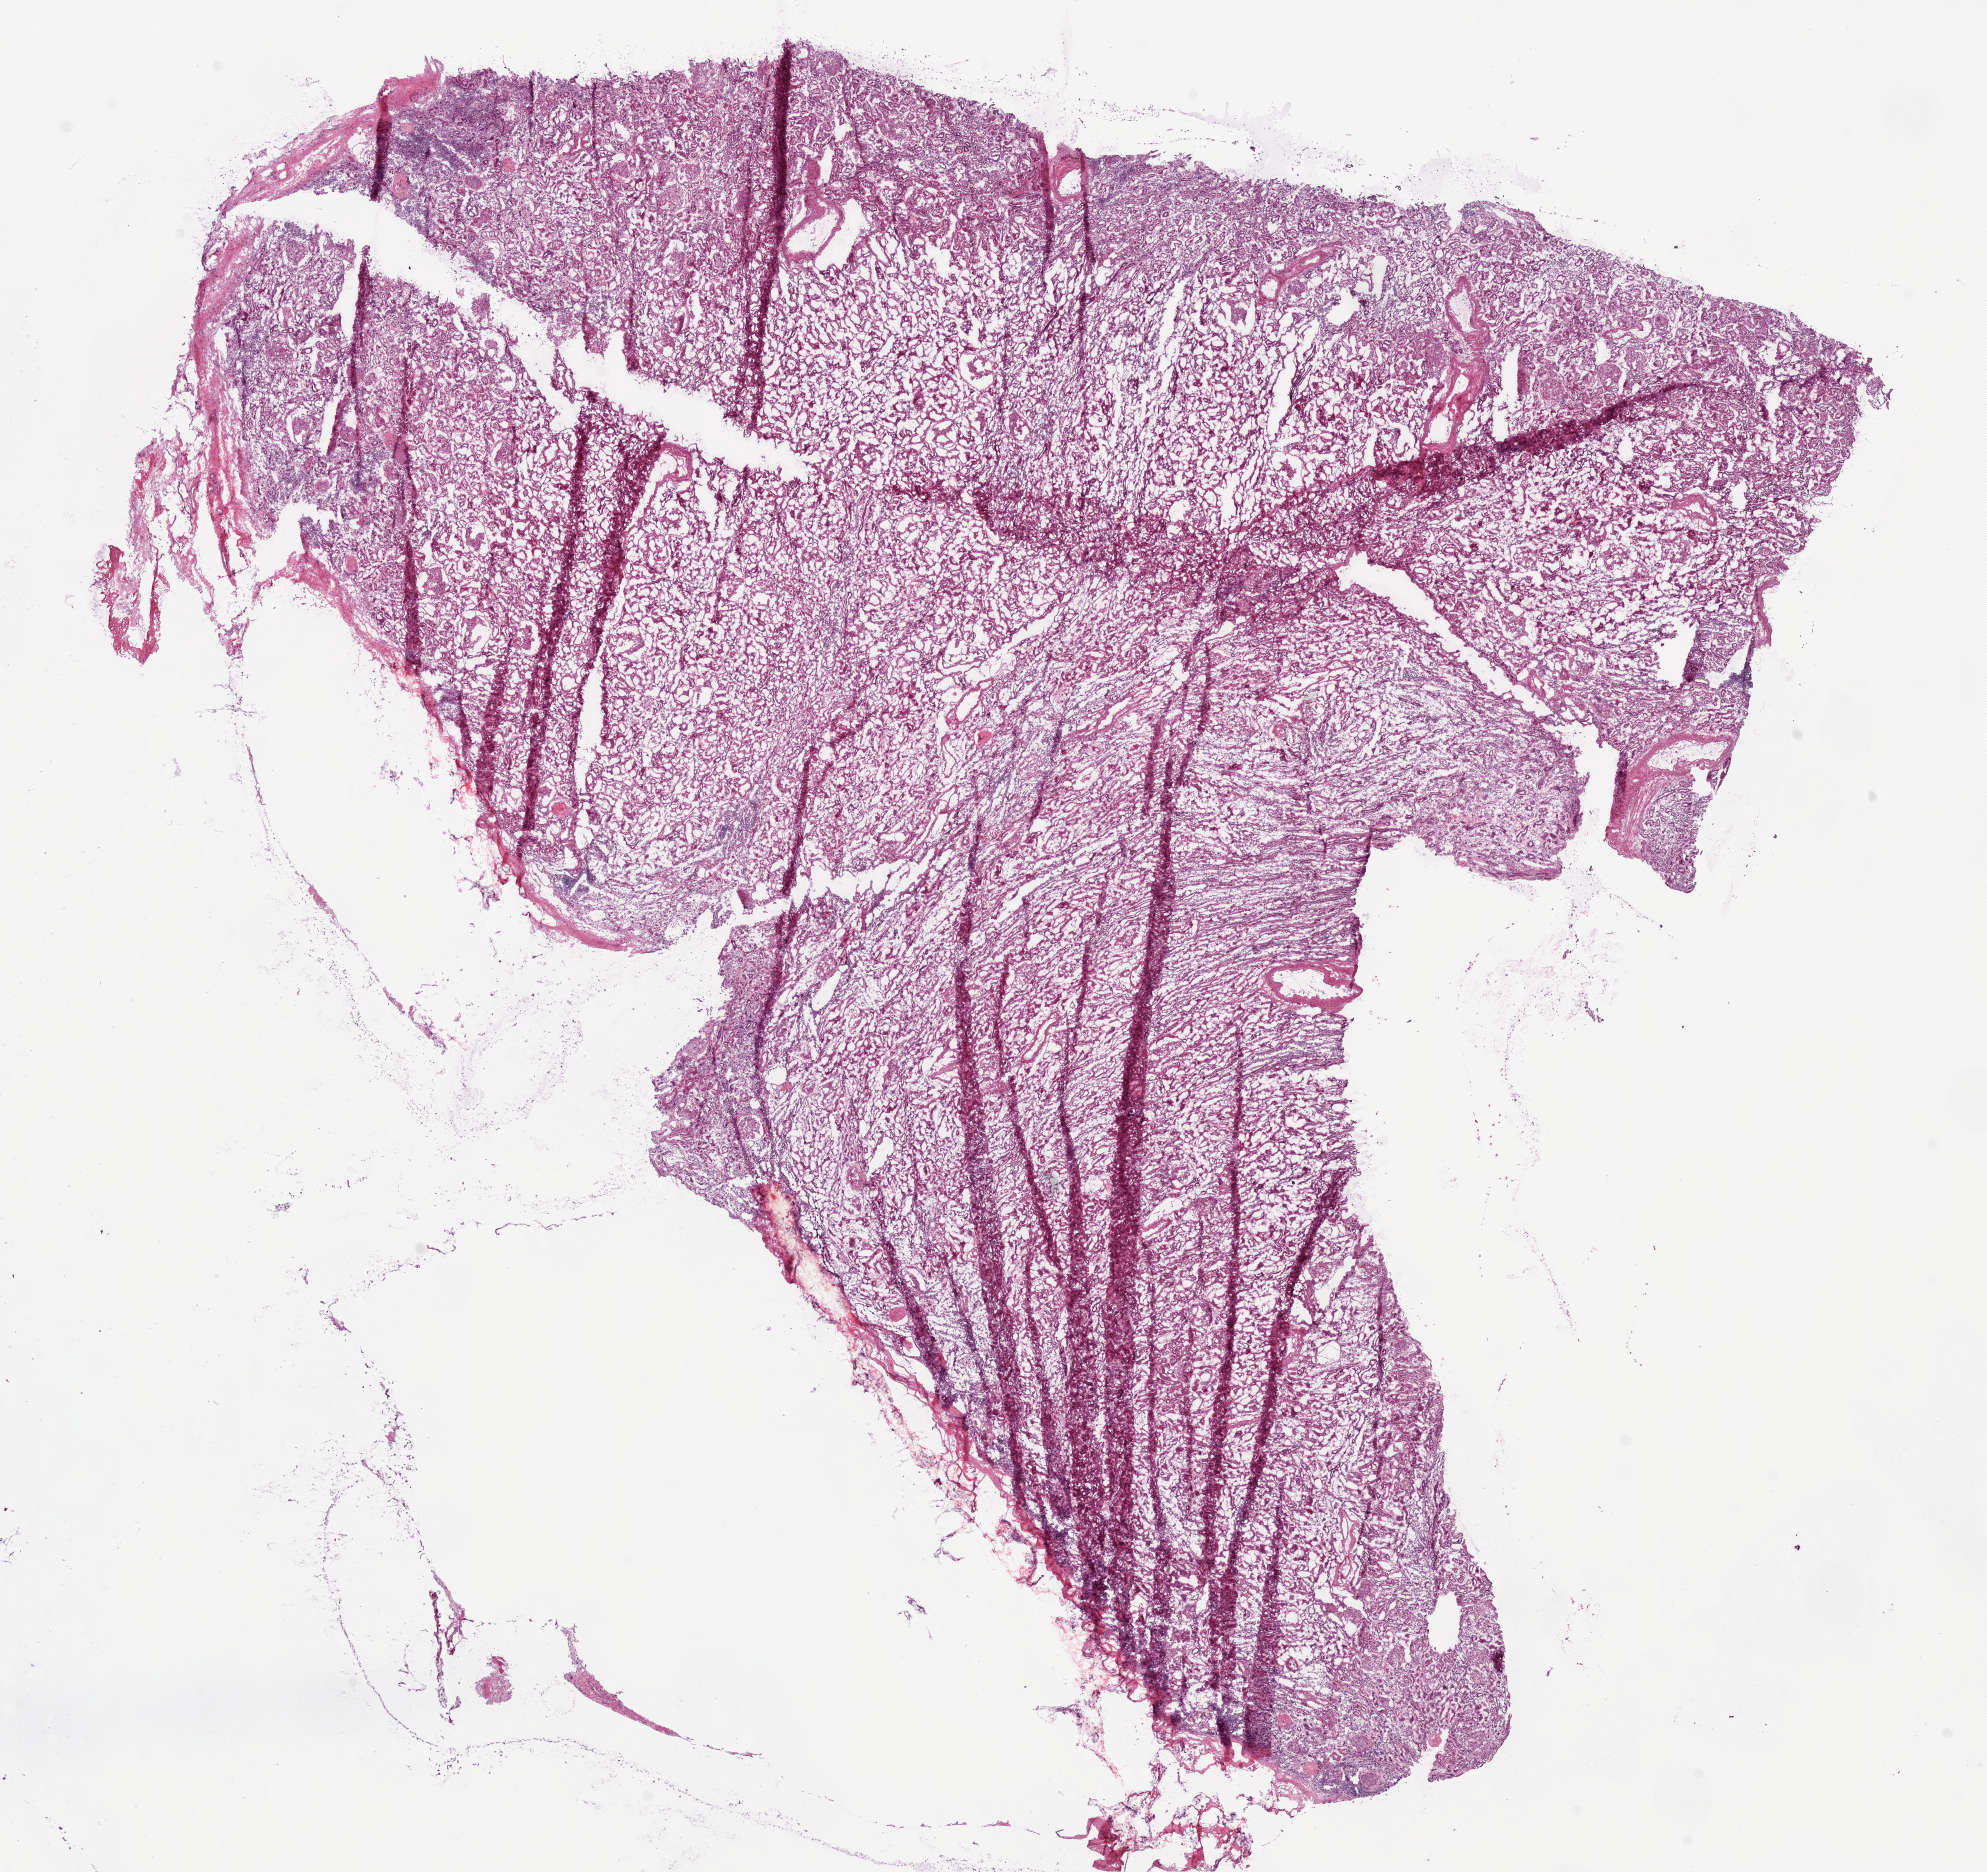
H&E whole-slide image — low-resolution overview of the scanned area, about 15.9 x 15.0 mm; frozen section from the top of the tissue portion; kidney, solid tissue normal (non-tumour tissue) sample. Female, age 59 years at initial diagnosis.
This section: solid tissue normal sample (biorepository sample class). Patient diagnosis: Clear cell adenocarcinoma, NOS.